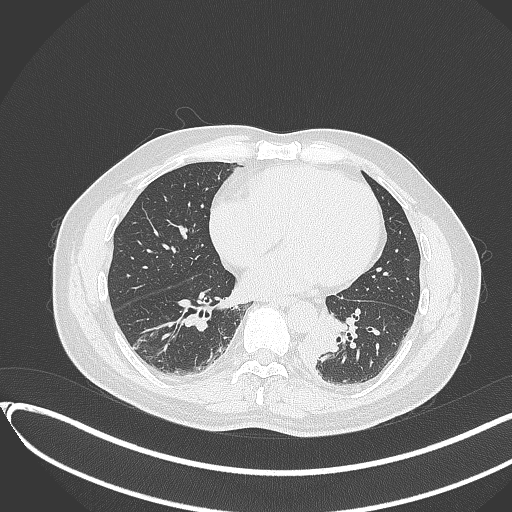
Chest CT, one axial slice. Position 128 of 417 along the scan axis. 120 kVp. Lung window (W 1500 / L -600 HU). 1 mm slice thickness. 512 × 512 image matrix. Male patient, age 54 years. From the clinical record (not read from this slice): clinical TNM (as recorded): T3 N0 M0.
Outlined on this slice (bounding box drawn by a radiologist):
- lung tumour (recorded histology: squamous cell carcinoma): bounding box (x1, y1, x2, y2) in pixels: (293, 307, 344, 364)